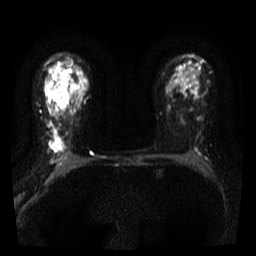
Breast MRI, one axial slice. Slice 25 of 36 in the series (ordered by position). Diffusion-weighted series; image 2 of 4 stored at this slice position (different b-values; order by instance number). 3 T. 256 × 256 image matrix. Female patient.
Annotated regions visible in this slice (manually delineated by an expert):
- tumour on diffusion-weighted imaging: box from (x=51, y=127) to (x=63, y=149) px